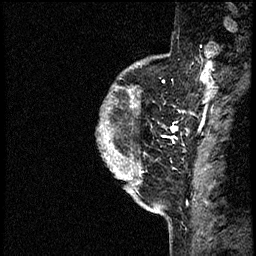
Breast MRI (dynamic contrast-enhanced), one sagittal slice; position 49 of 60 along the scan axis; dynamic contrast-enhanced study with each time point stored as its own series, time point 2 of 4 at this slice position (early post-contrast, ordered by acquisition time); 1.5 T; TE 4.2 ms, TR 17.6 ms; 256 × 256 image matrix. Female patient, age 40 years. Case-level facts recorded for this patient, not image findings: setting: breast cancer imaged before/during neoadjuvant chemotherapy; receptor status: HER2-positive.
Annotated regions visible in this slice (semi-automatic segmentation, software-assisted and operator-edited):
- analysis volume of interest (the breast-tissue region the enhancement analysis was run in; not a lesion): bounding box [x1, y1, x2, y2] px = [97, 56, 197, 205]
- tumour enhancement mask (voxels above the 100 % enhancement threshold inside the analysis volume of interest): [105, 101, 178, 175]